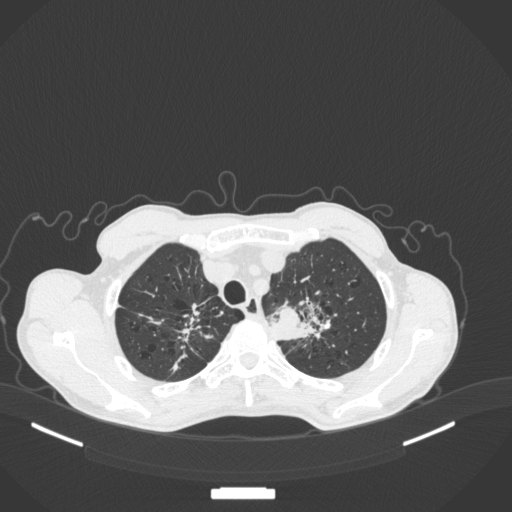
Chest CT, one axial slice. Slice 359 of 394 in the series (ordered by position). Reconstruction kernel B31f. Lung window (W 1500 / L -600 HU). 1 mm slice thickness. 512 × 512 image matrix, field of view 400 × 400 mm. Patient: male, 65 years. Case-level facts recorded for this patient, not image findings: clinical TNM (as recorded): T2b N0 M0; histopathological grade: G2.
Outlined on this slice (bounding box drawn by a radiologist):
- lung tumour (recorded histology: adenocarcinoma): bounding box <267,296,330,341> (left, top, right, bottom; pixels)